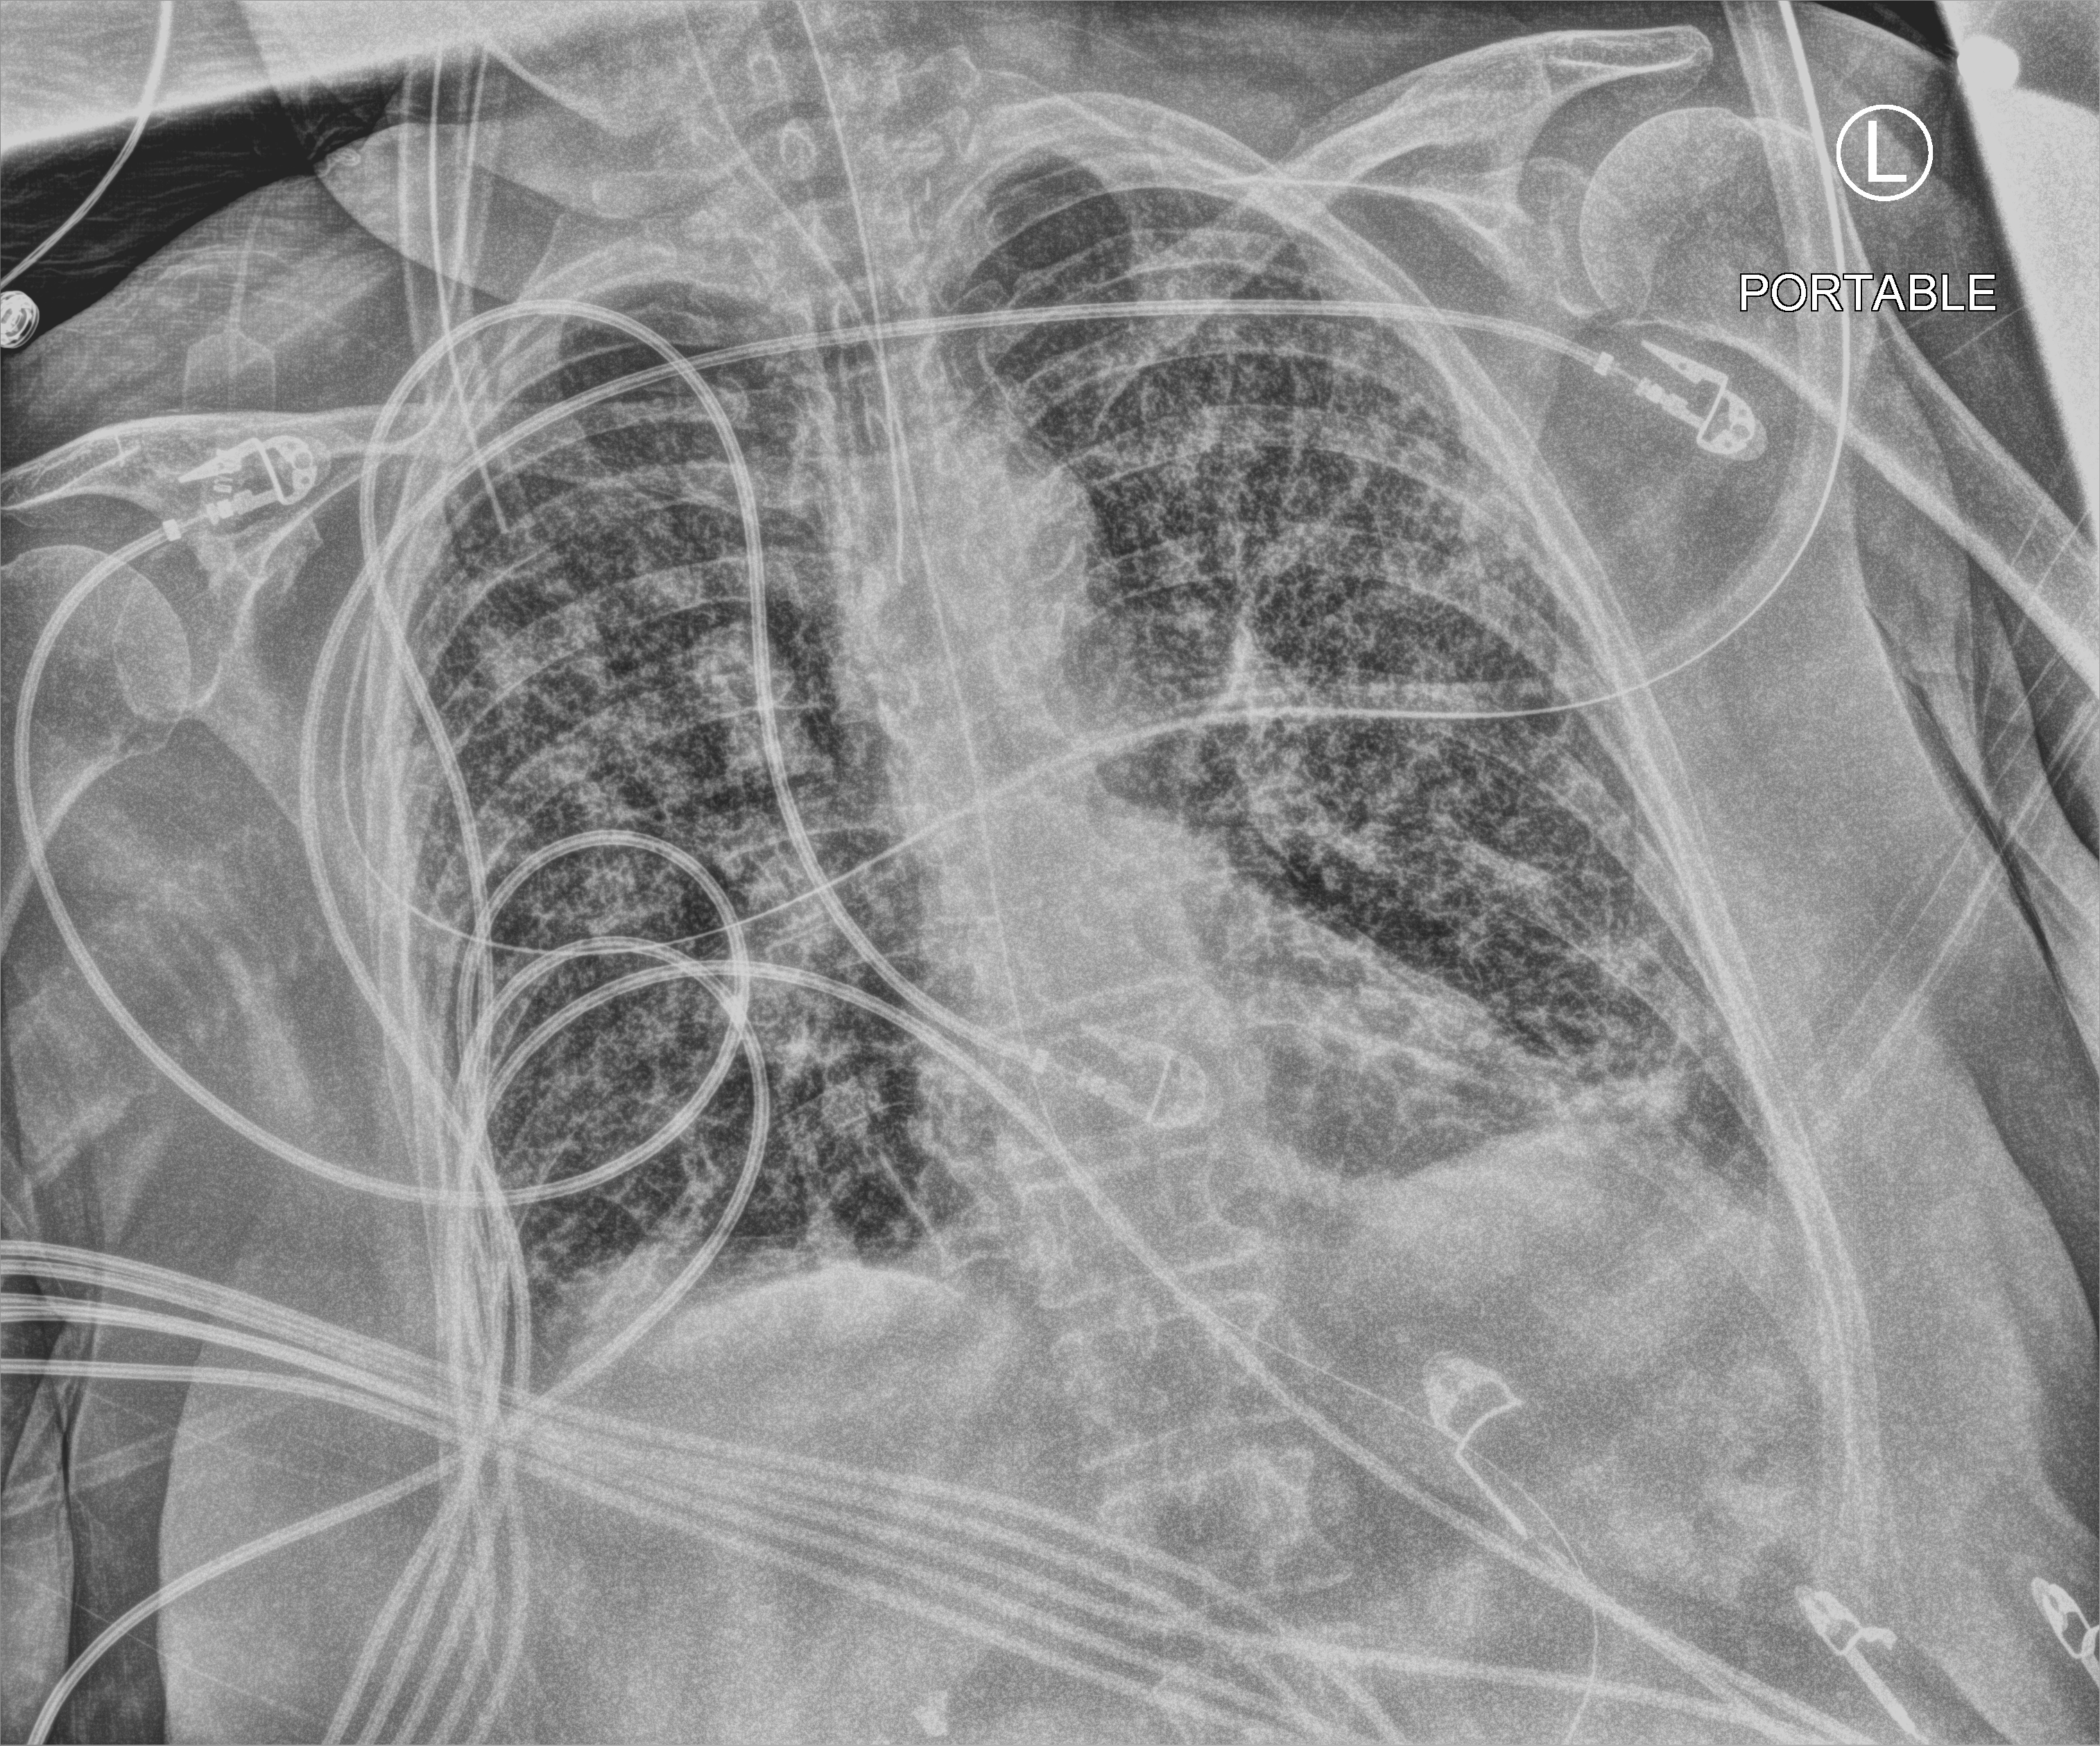
Portable chest radiograph; anteroposterior (AP) projection. Patient hospitalised with COVID-19; female, aged 60–74 years.
Admission-level facts for this patient (not findings on this image; timing relative to this image not recorded): admitted to intensive care during this hospital stay: yes; mechanically ventilated during this hospital stay: yes.